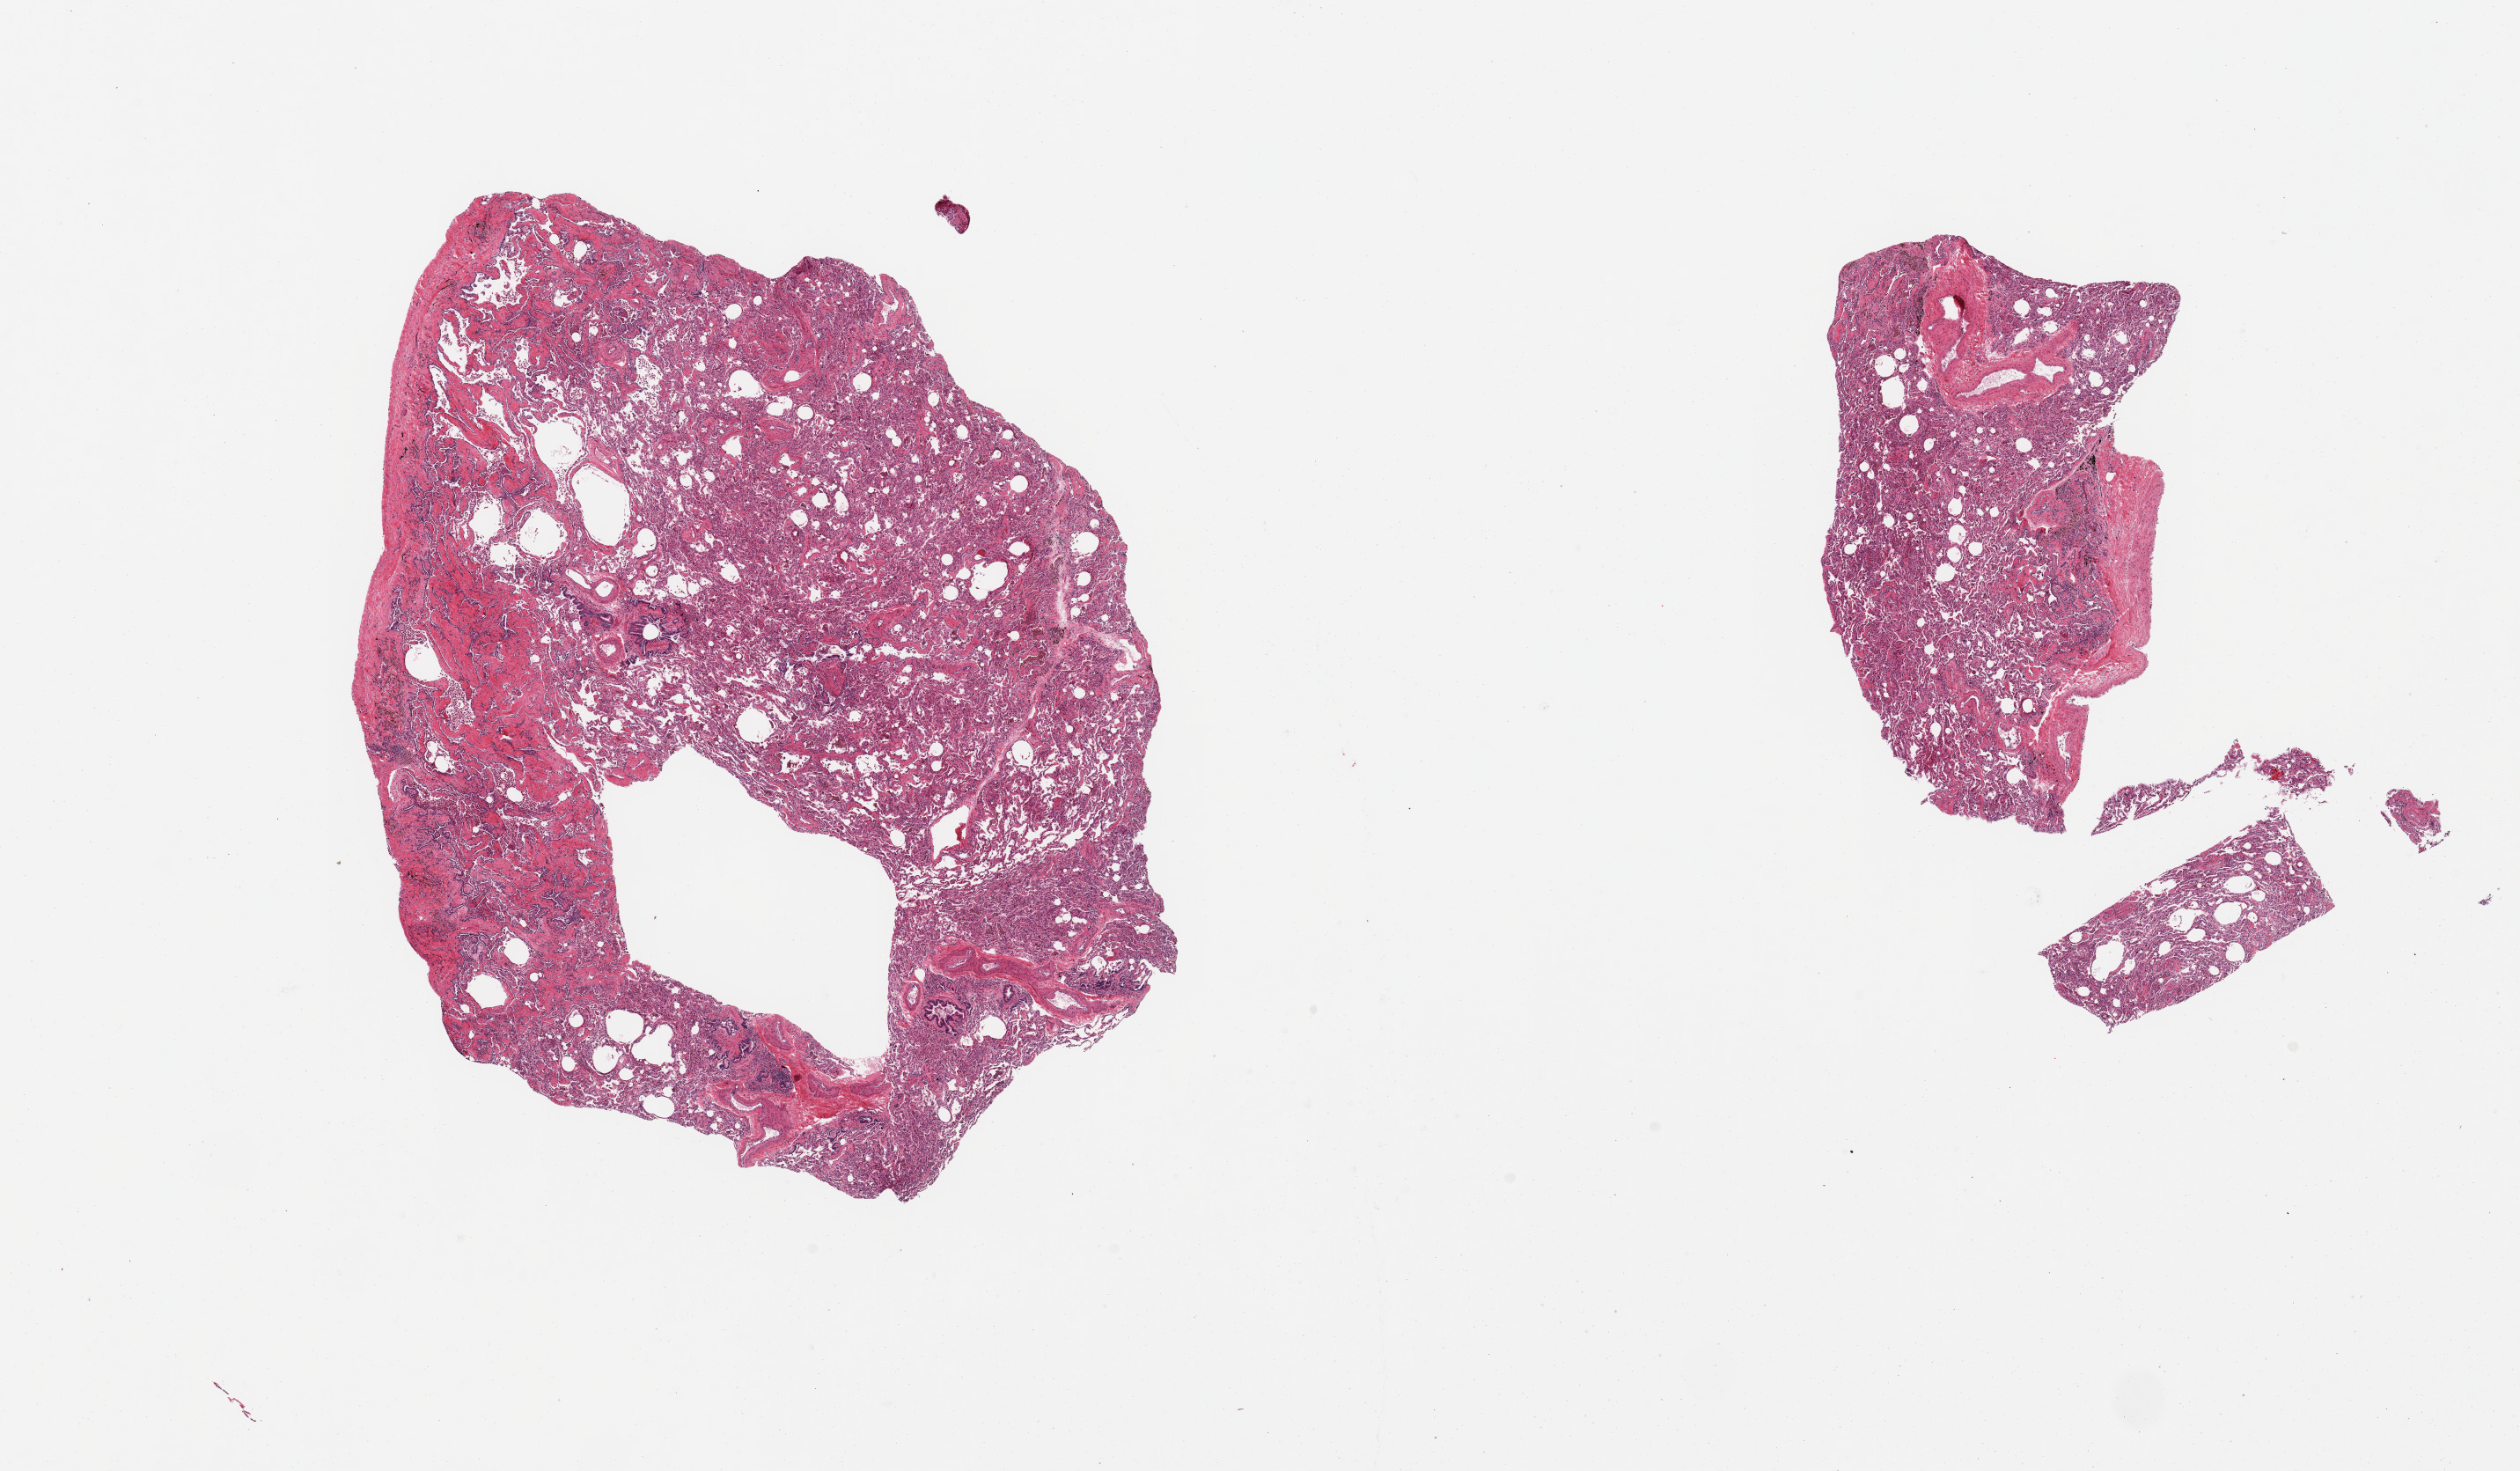
Whole-slide image, H&E stain — whole scanned area (about 22.6 x 13.2 mm) shown as a low-resolution overview, PAXgene-fixed paraffin-embedded (PFPE) section, sampled site (target tissue): lung, tissue donor sample. Donor sex: male.
Reviewer comment on this tissue sample: 2 pieces; fibrosis, emphysema, pigmented macrophages.